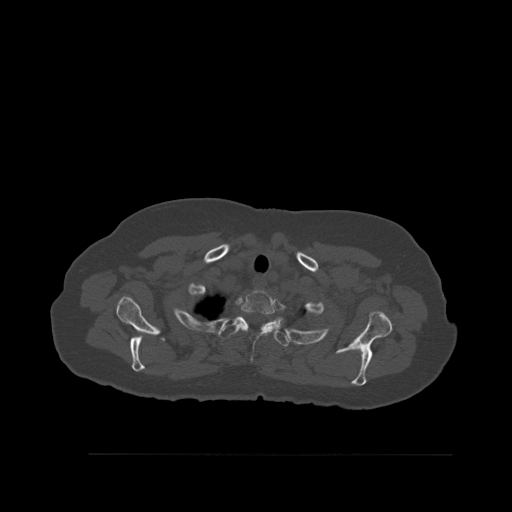
CT including the spine, one axial slice. Position 438 of 527 along the scan axis. Bone window (W 1800 / L 400 HU). 1.5 mm slice thickness. 512 × 512 image matrix, field of view 470 × 470 mm. Female patient, age 73 years. Case-level facts recorded for this patient, not image findings: primary cancer: breast.
Annotated regions visible in this slice (semi-automatic segmentation, software-assisted and operator-edited):
- T1 vertebra: box from (x=241, y=290) to (x=275, y=333) px
- T2 vertebra: (x=218, y=316)–(x=290, y=347)